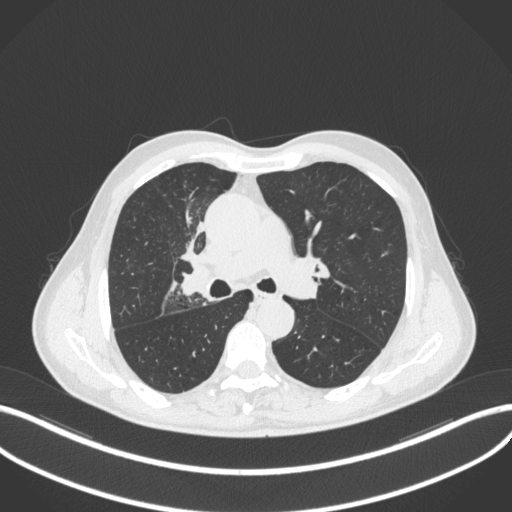
Chest CT, one axial slice. Slice 301 of 490 in the series (ordered by position). Reconstruction kernel B31f. 120 kVp. Lung window (W 1500 / L -600 HU). 512 × 512 image matrix. Patient: male, 69 years. From the clinical record (not read from this slice): clinical TNM (as recorded): T2a N0 M0.
Annotated regions visible in this slice (rectangle marked by the reading radiologist):
- lung tumour (recorded histology: adenocarcinoma): box from (x=177, y=260) to (x=208, y=299) px